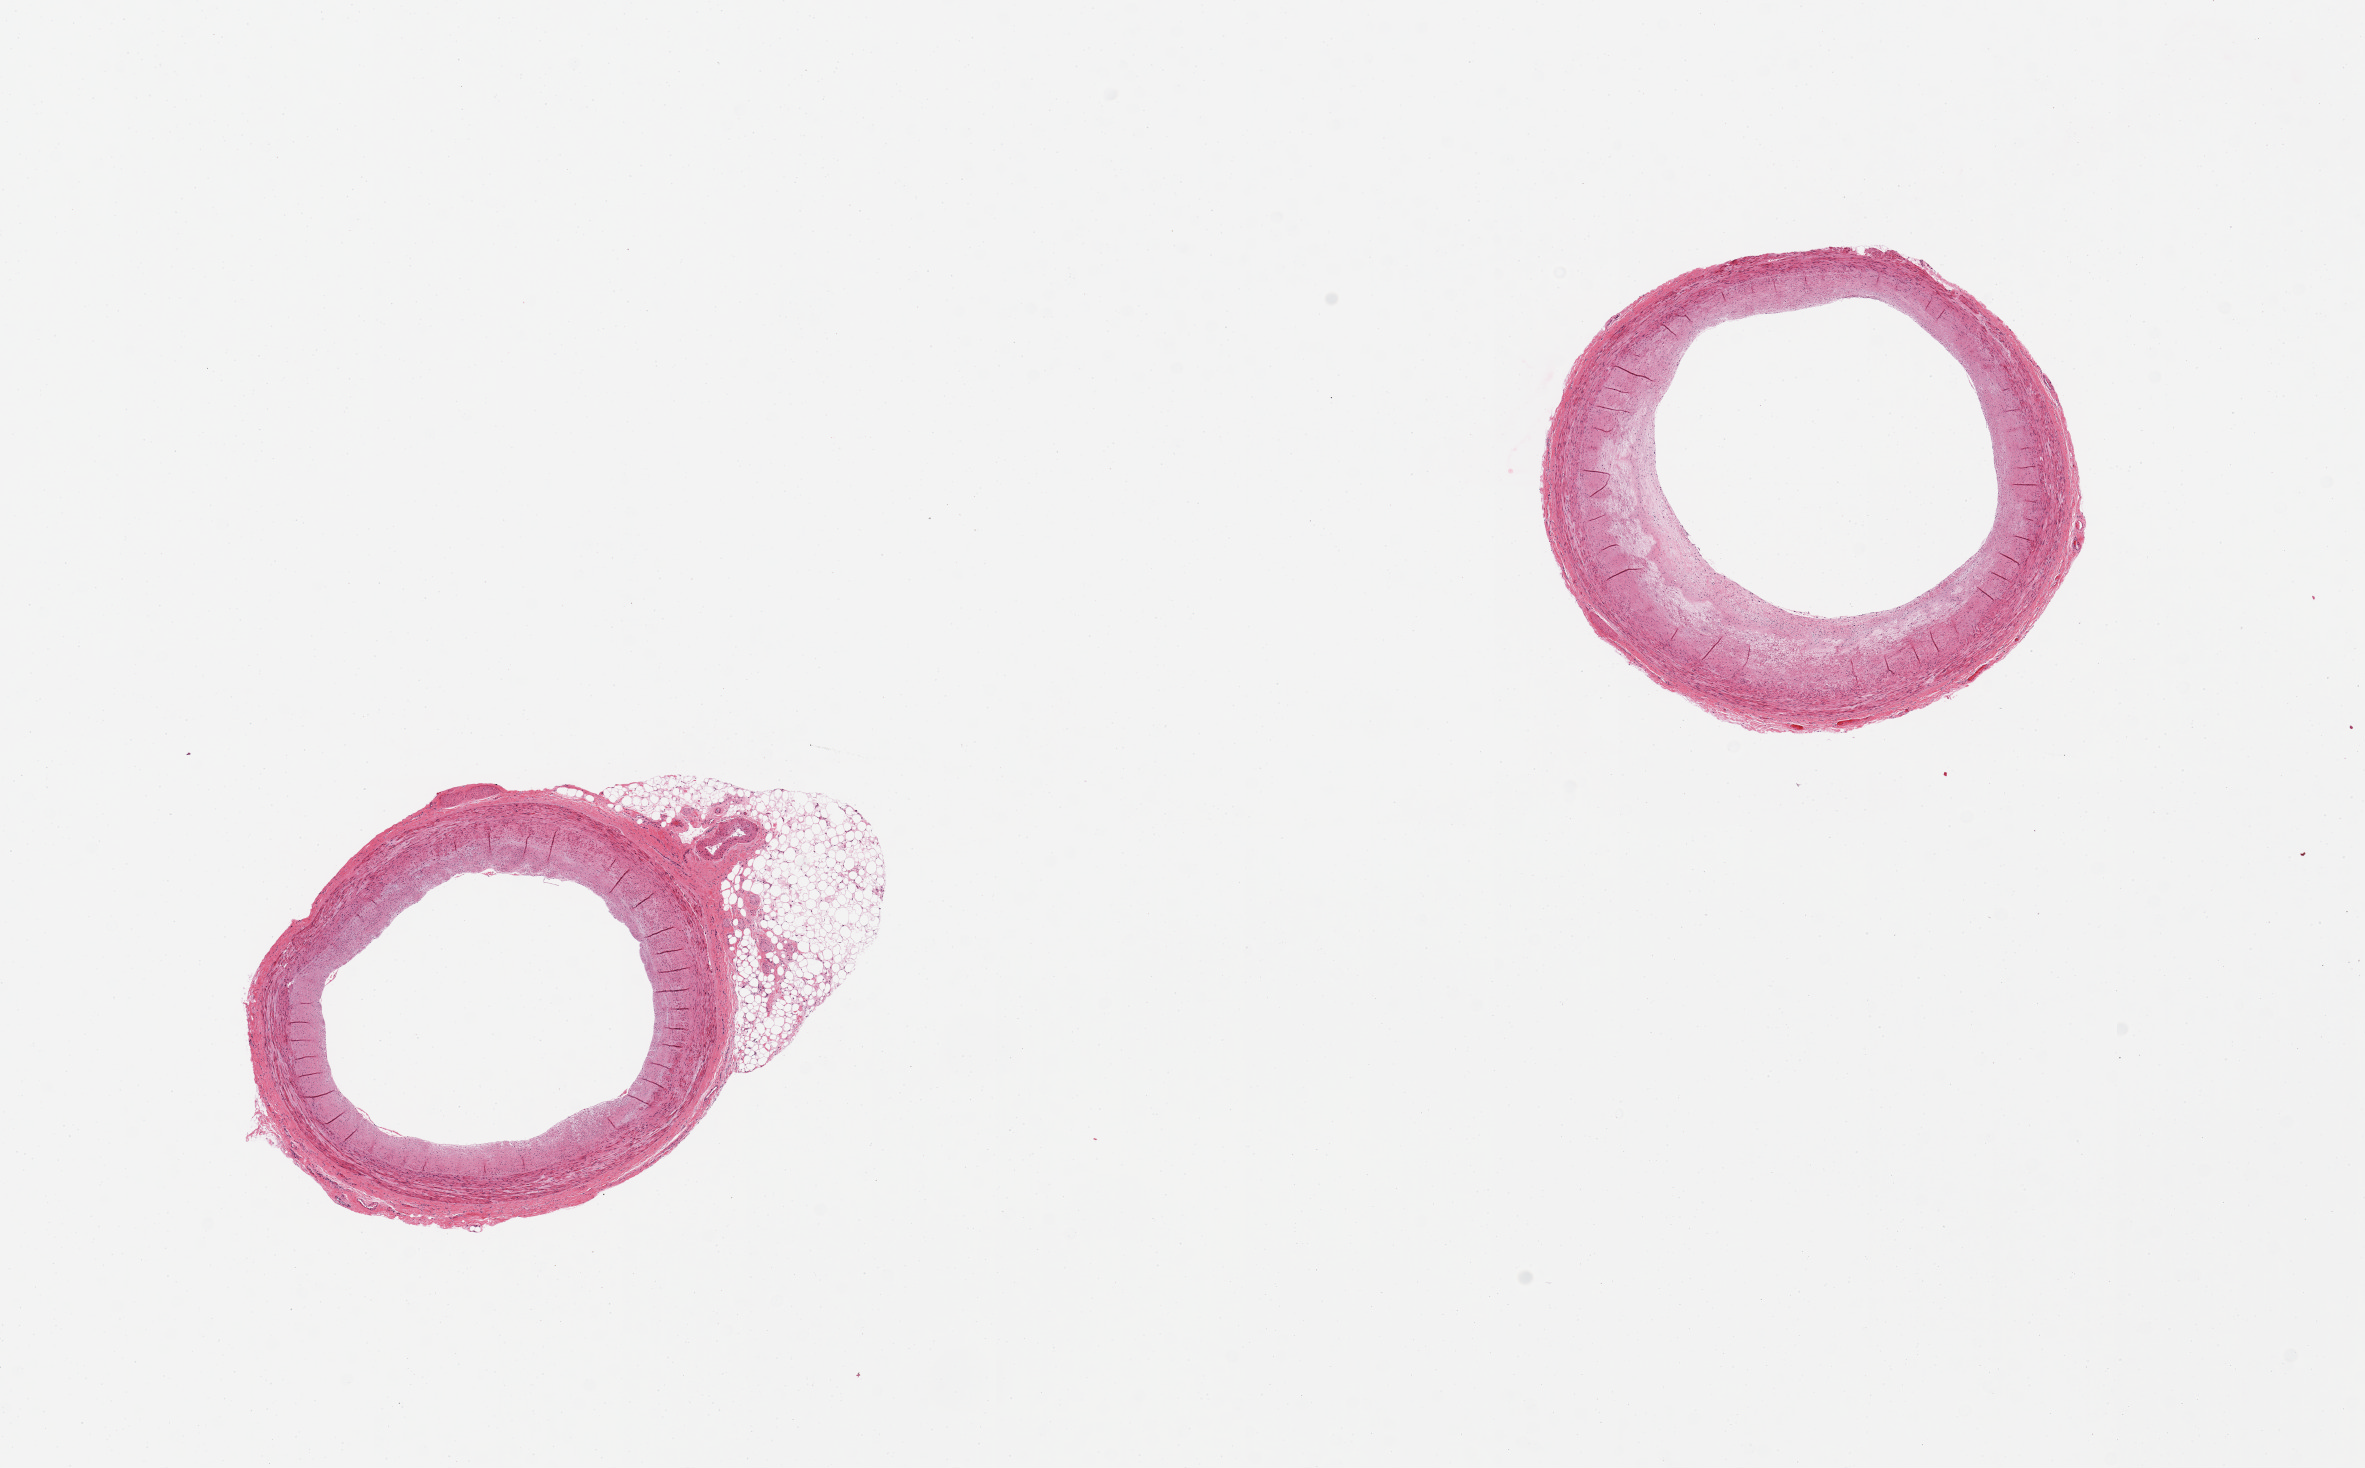
Haematoxylin and eosin whole-slide image, brightfield, a low-resolution overview of the entire scanned area, about 18.7 x 11.6 mm (from a 20x scan); PAXgene-fixed paraffin-embedded (PFPE) section; target tissue: coronary artery; donor tissue sample. Donor sex: male.
- review note (as recorded): 2 pieces, clean specimens; nubbin of adherent fat on one ~1.5mm